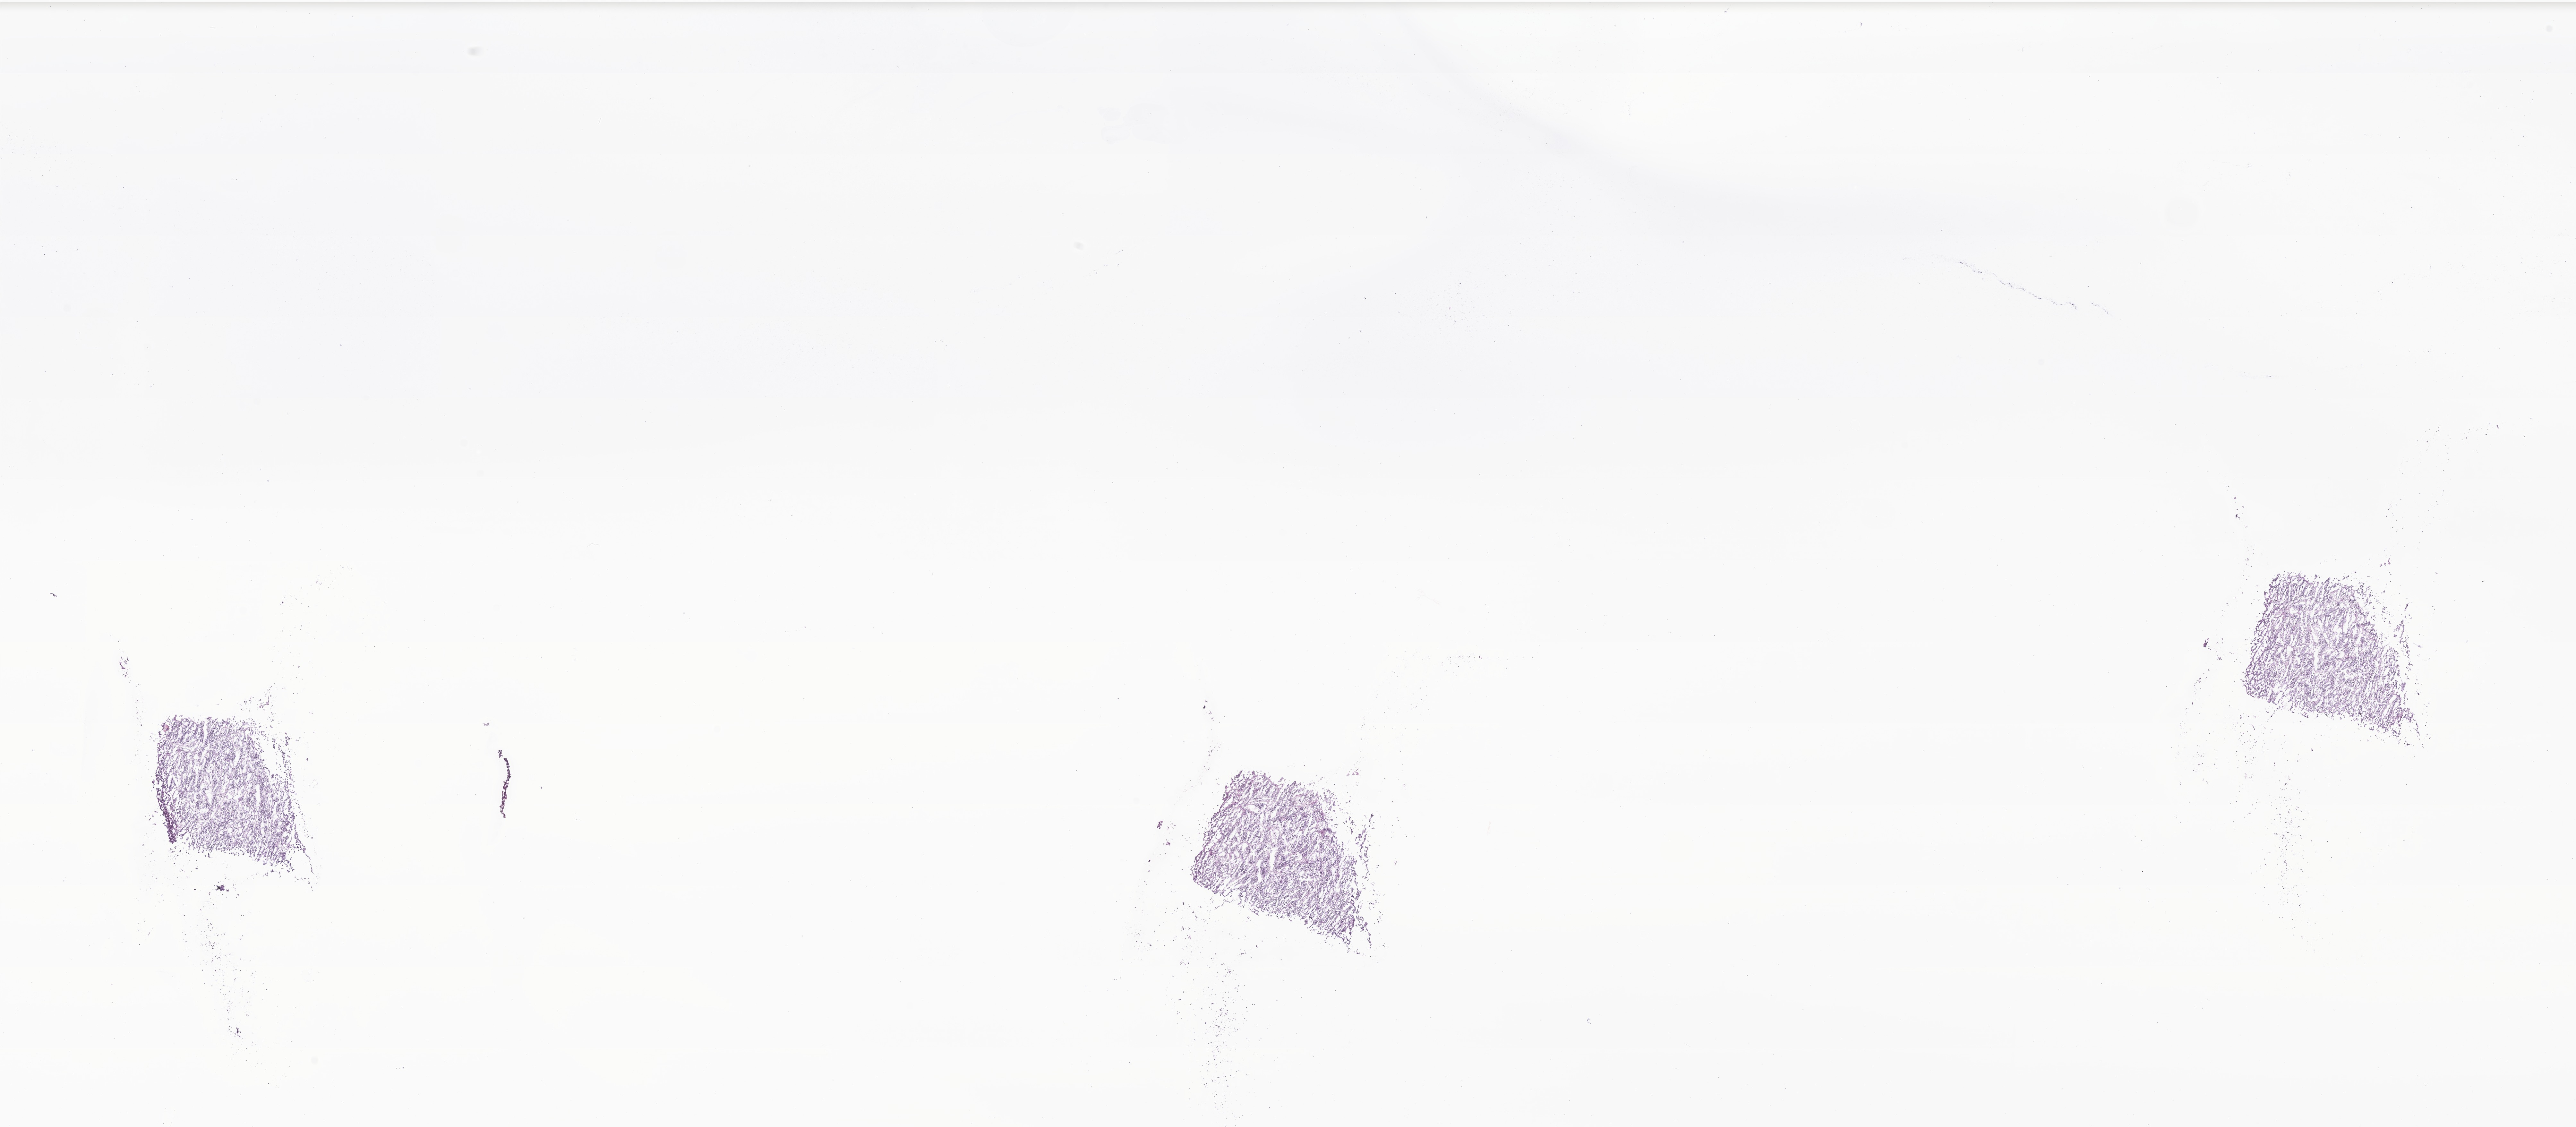
H&E whole-slide image of tumor tissue from the adrenal gland, whole scanned area (about 33.9 x 14.8 mm) shown as a low-resolution overview, frozen section. Patient male; age 60 days.
Diagnosis: Neuroblastoma, NOS.